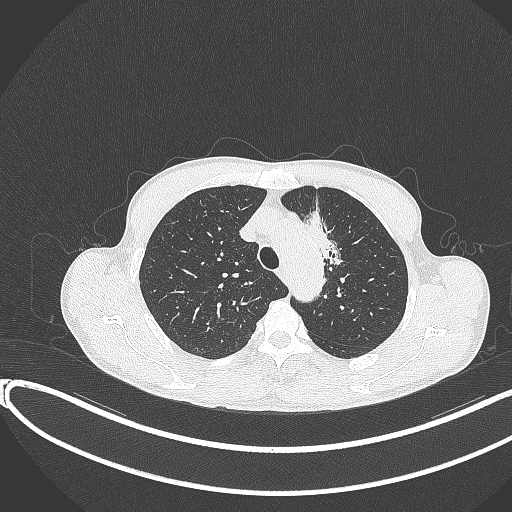
Chest CT, one axial slice; position 294 of 374 along the scan axis; 120 kVp; lung window (W 1500 / L -600 HU); 1 mm slice thickness; 512 × 512 image matrix, field of view 400 × 400 mm. Male patient, age 58 years. Case-level facts recorded for this patient, not image findings: clinical TNM (as recorded): T1c N1 M0.
Annotated regions visible in this slice (bounding box drawn by a radiologist):
- lung tumour (recorded histology: adenocarcinoma): box from (x=292, y=199) to (x=351, y=271) px